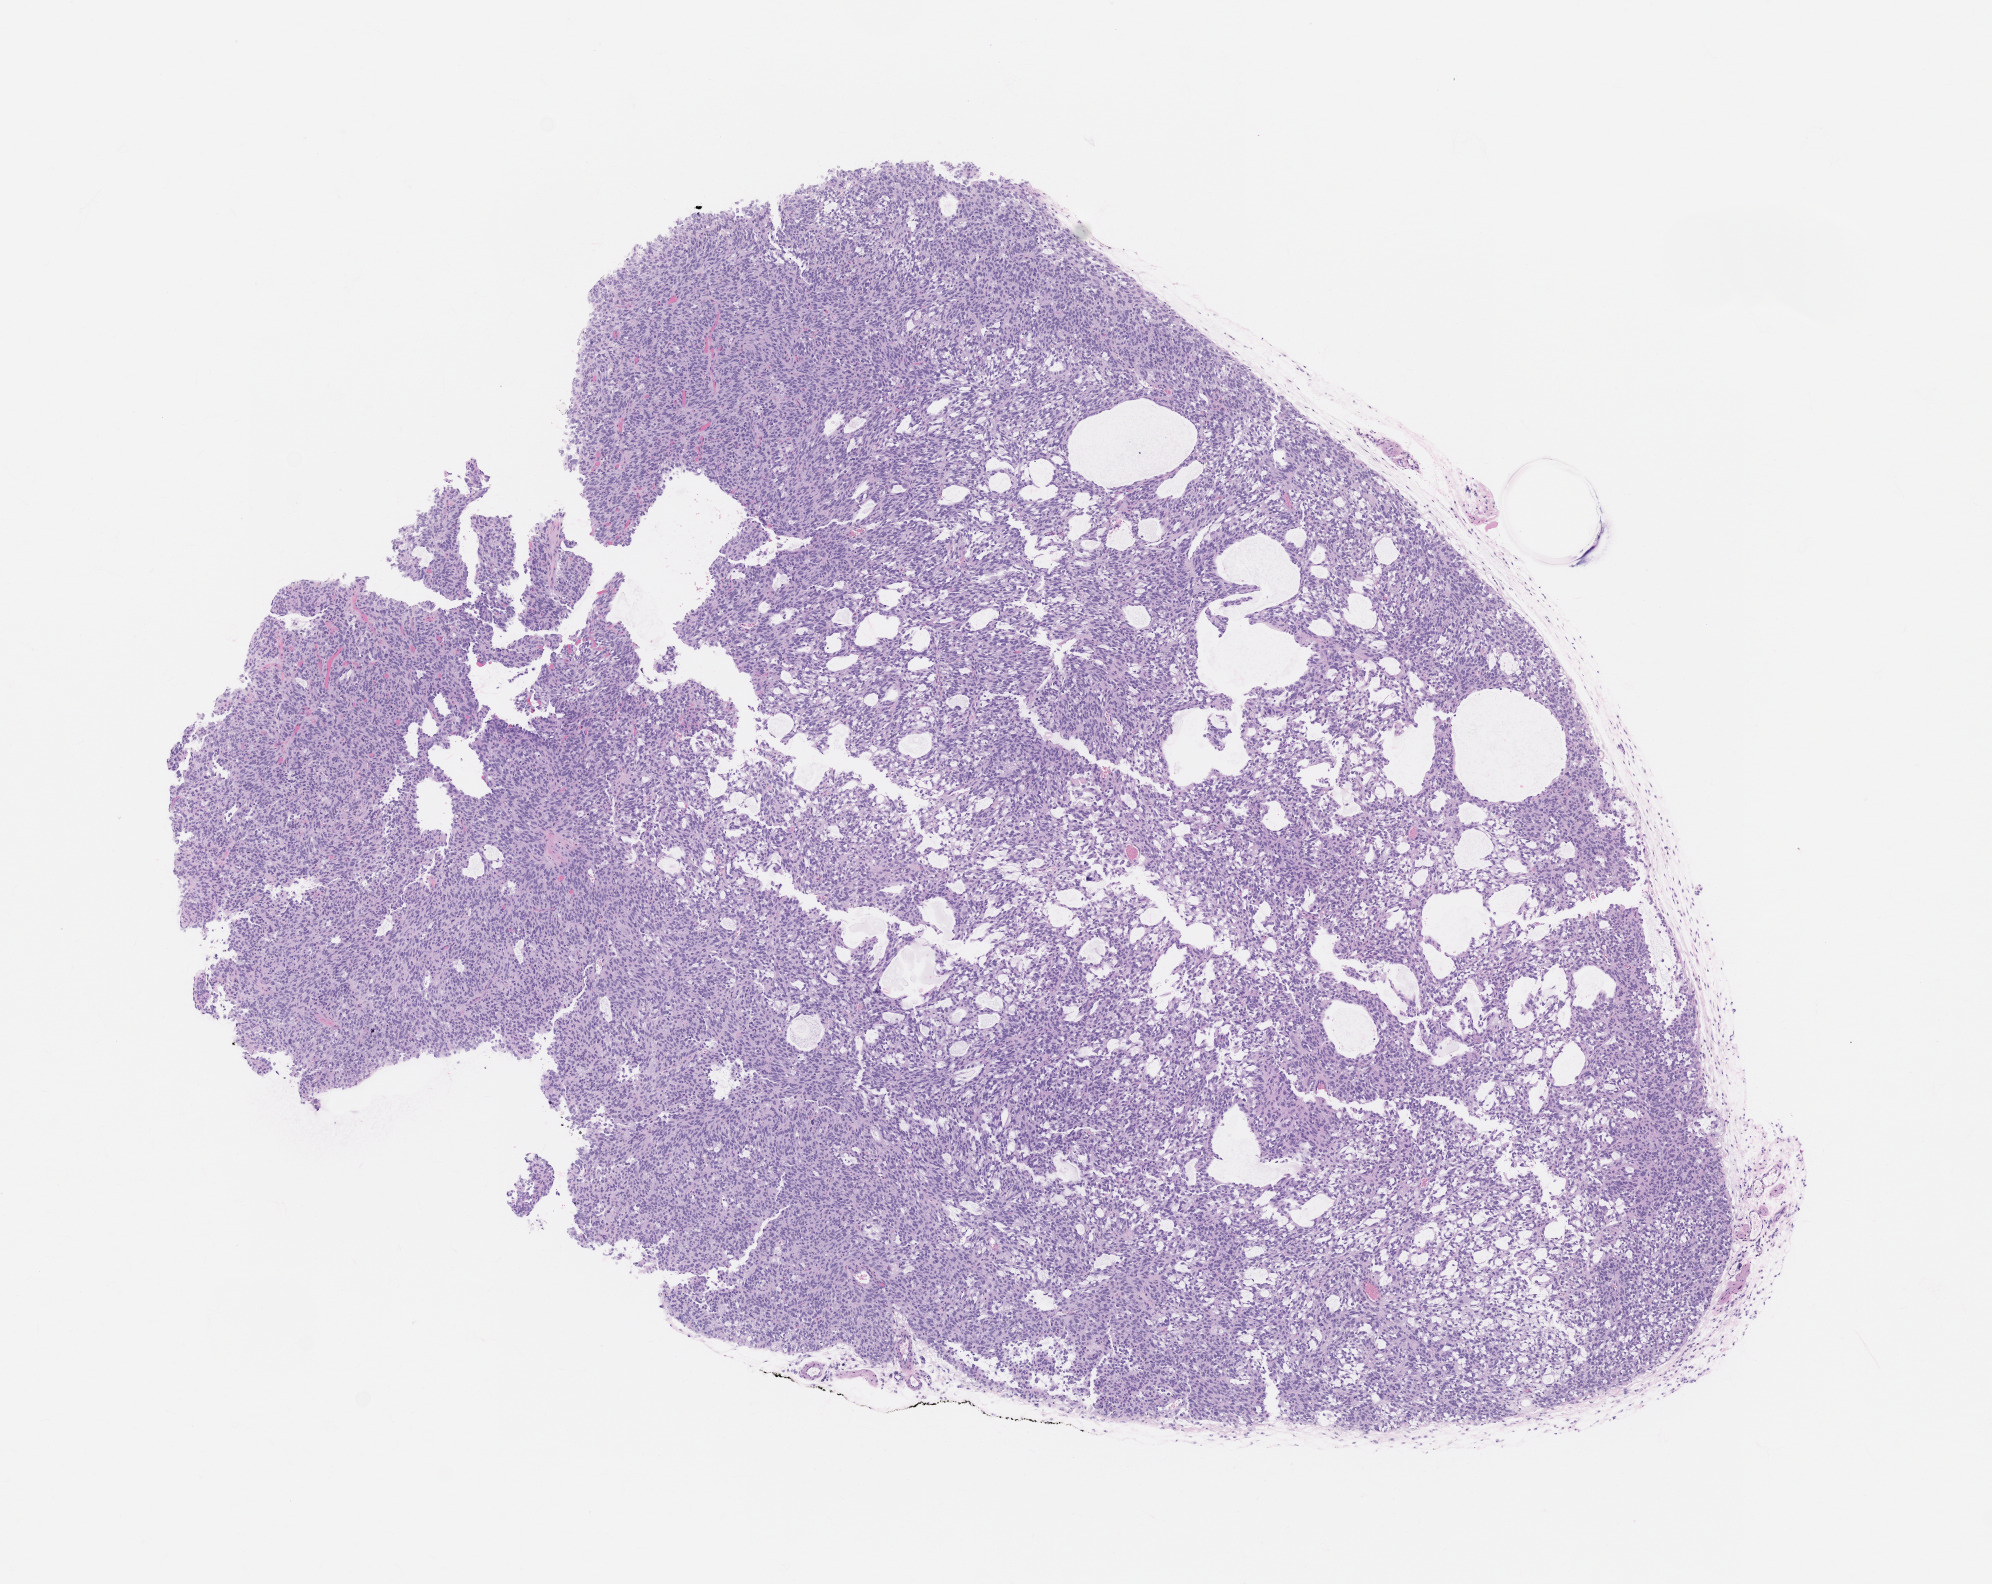
Whole-slide image, H&E: patient-derived xenograft (human tumor grown in a mouse), passage 0, low-resolution overview of the scanned area, about 8.0 x 6.4 mm, formalin-fixed, paraffin-embedded (FFPE) tissue, originating tumor site category: uterus.
Originating patient diagnosis: Leiomyosarcoma.